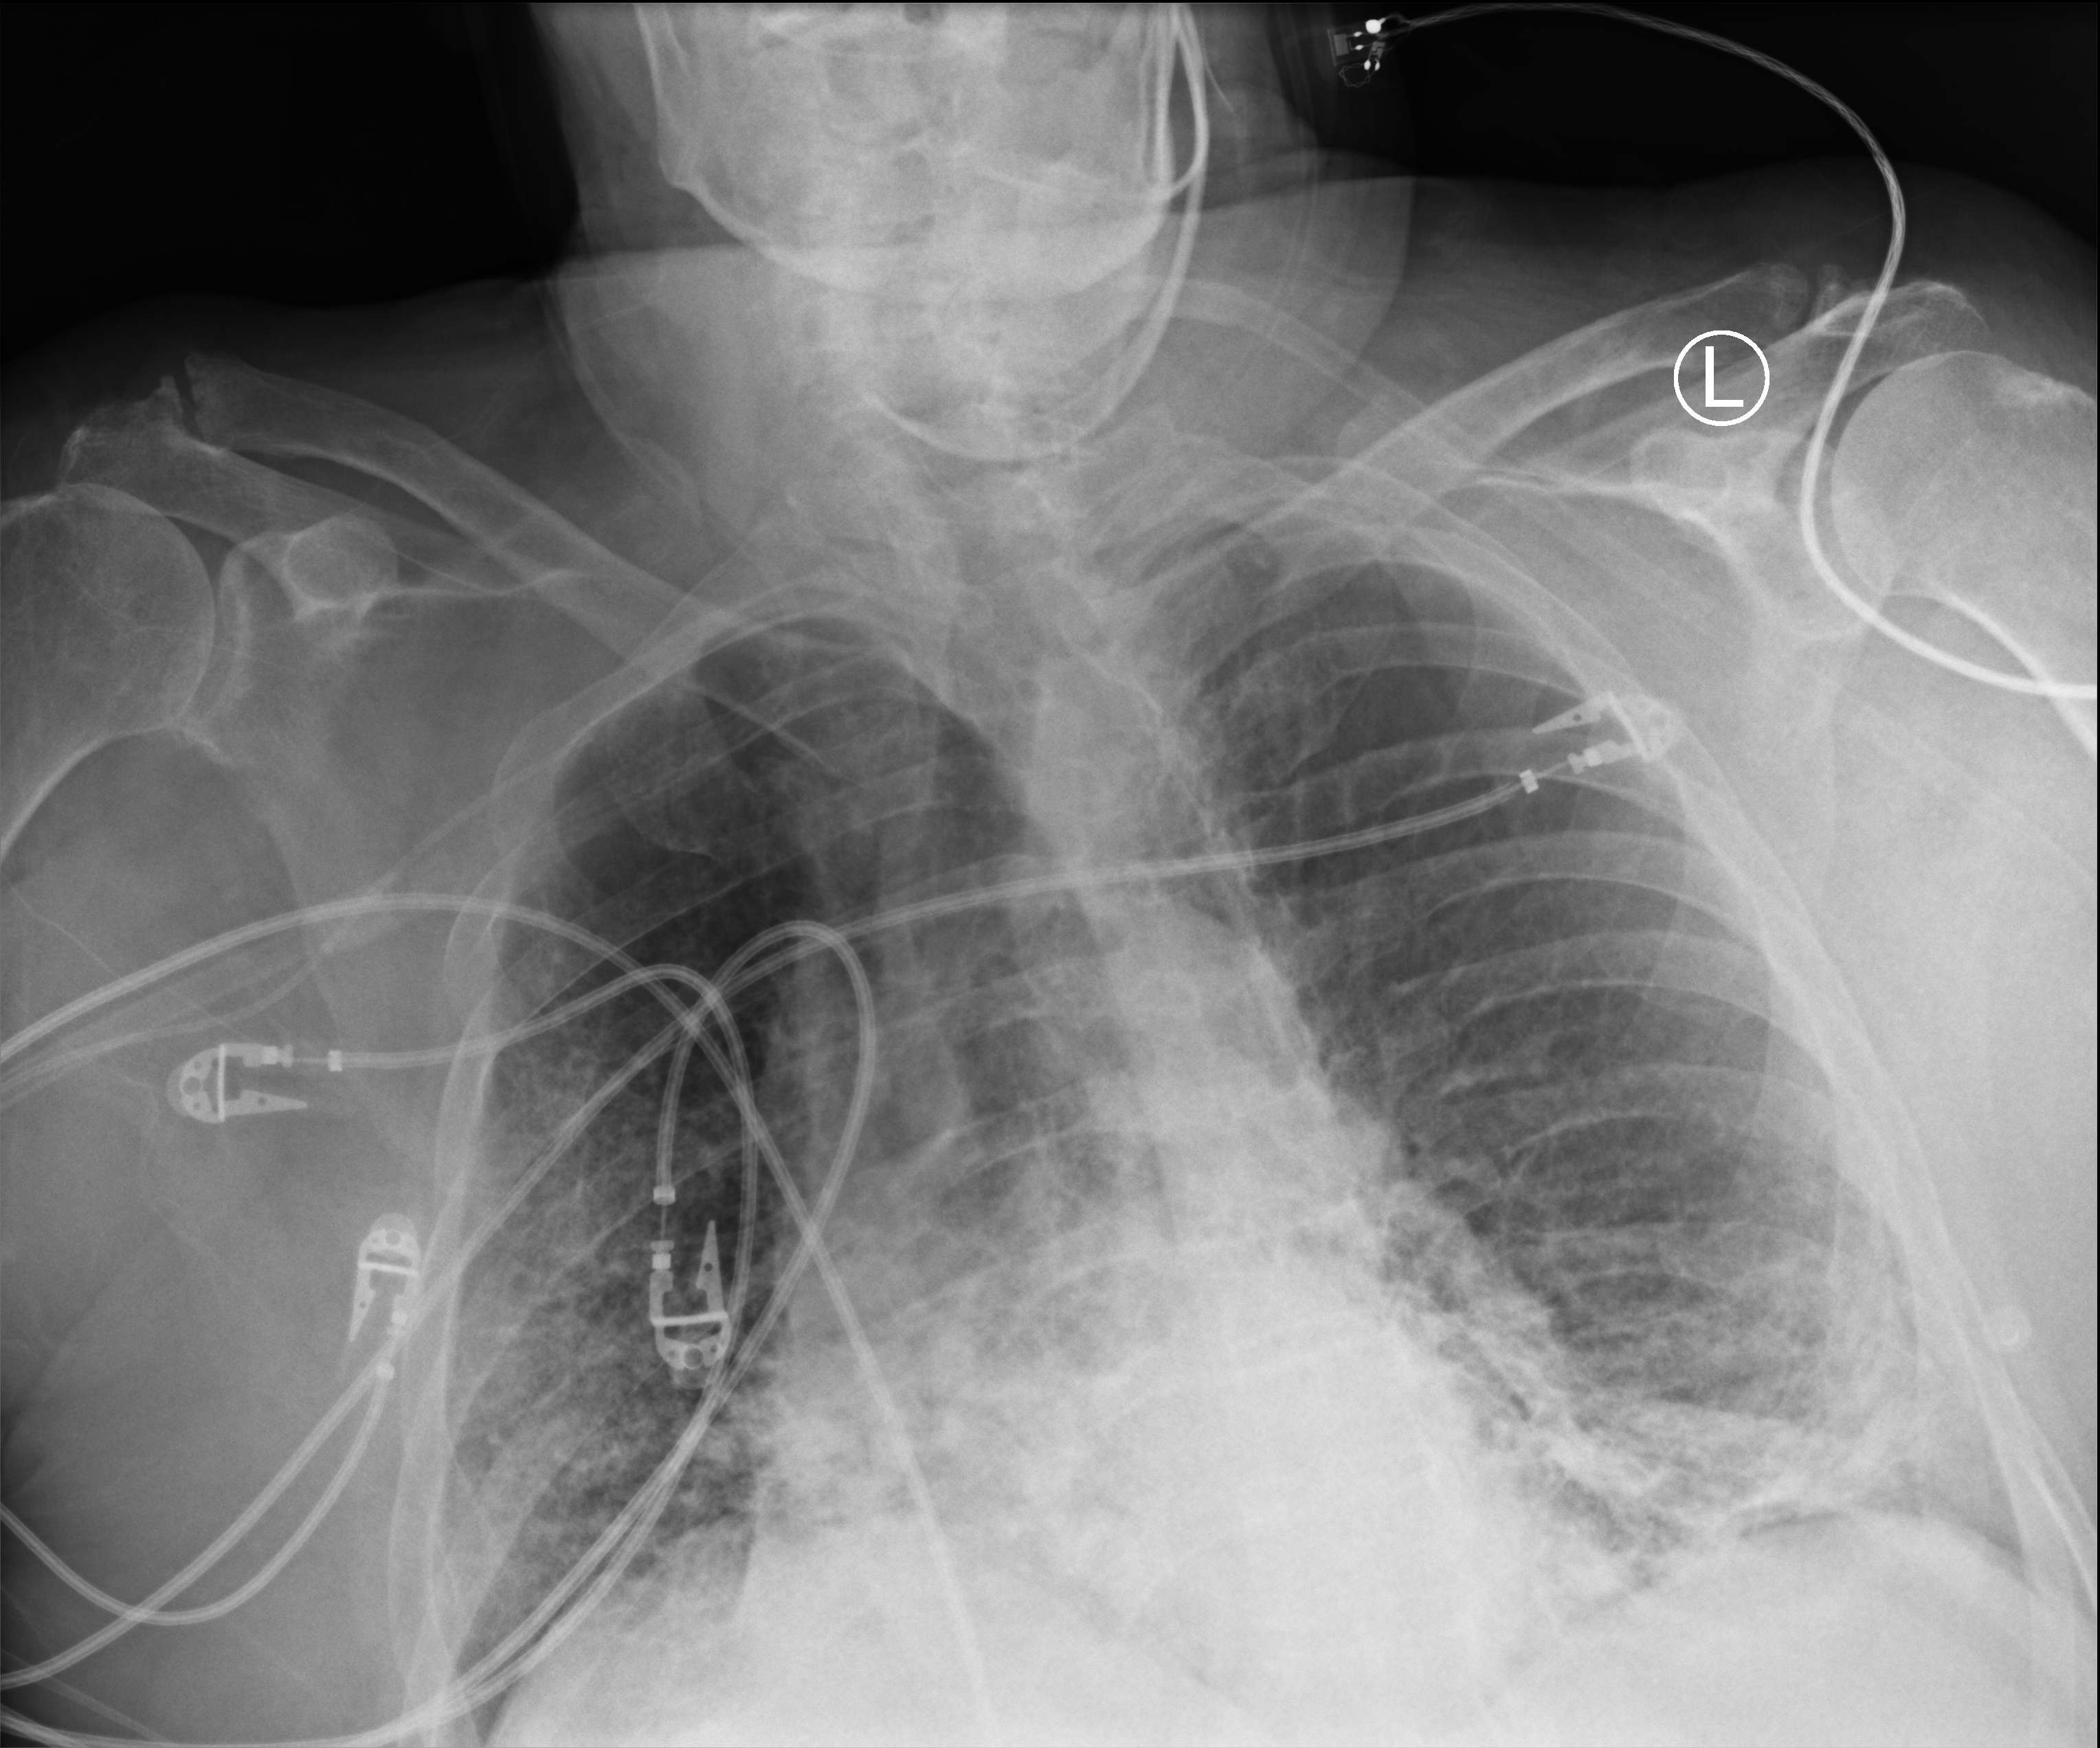
Chest X-ray (portable). Male patient hospitalised with COVID-19, age 60–74 years.
Hospital-stay facts (about this admission, not read from this image; timing relative to this image not recorded):
- smoking status (admission record): former
- diabetes (admission record): no